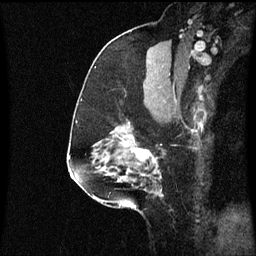
Breast MRI (dynamic contrast-enhanced), one sagittal slice. Slice 37 of 60 in the series (ordered by position). Dynamic contrast-enhanced series, image 2 of 3 at this slice position (ordered by acquisition). 1.5 T. TE 4.2 ms, TR 8.9 ms. 256 × 256 image matrix, field of view 200 × 200 mm. Patient: female, 58 years. Case-level facts recorded for this patient, not image findings: setting: breast cancer imaged before/during neoadjuvant chemotherapy; receptor status: triple-negative.
Outlined on this slice (semi-automatic segmentation, software-assisted and operator-edited):
- analysis volume of interest (the breast-tissue region the enhancement analysis was run in; not a lesion): bounding box [x1, y1, x2, y2] px = [104, 118, 165, 179]
- tumour enhancement mask (voxels above the 70 % enhancement threshold inside the analysis volume of interest): [104, 138, 157, 179]